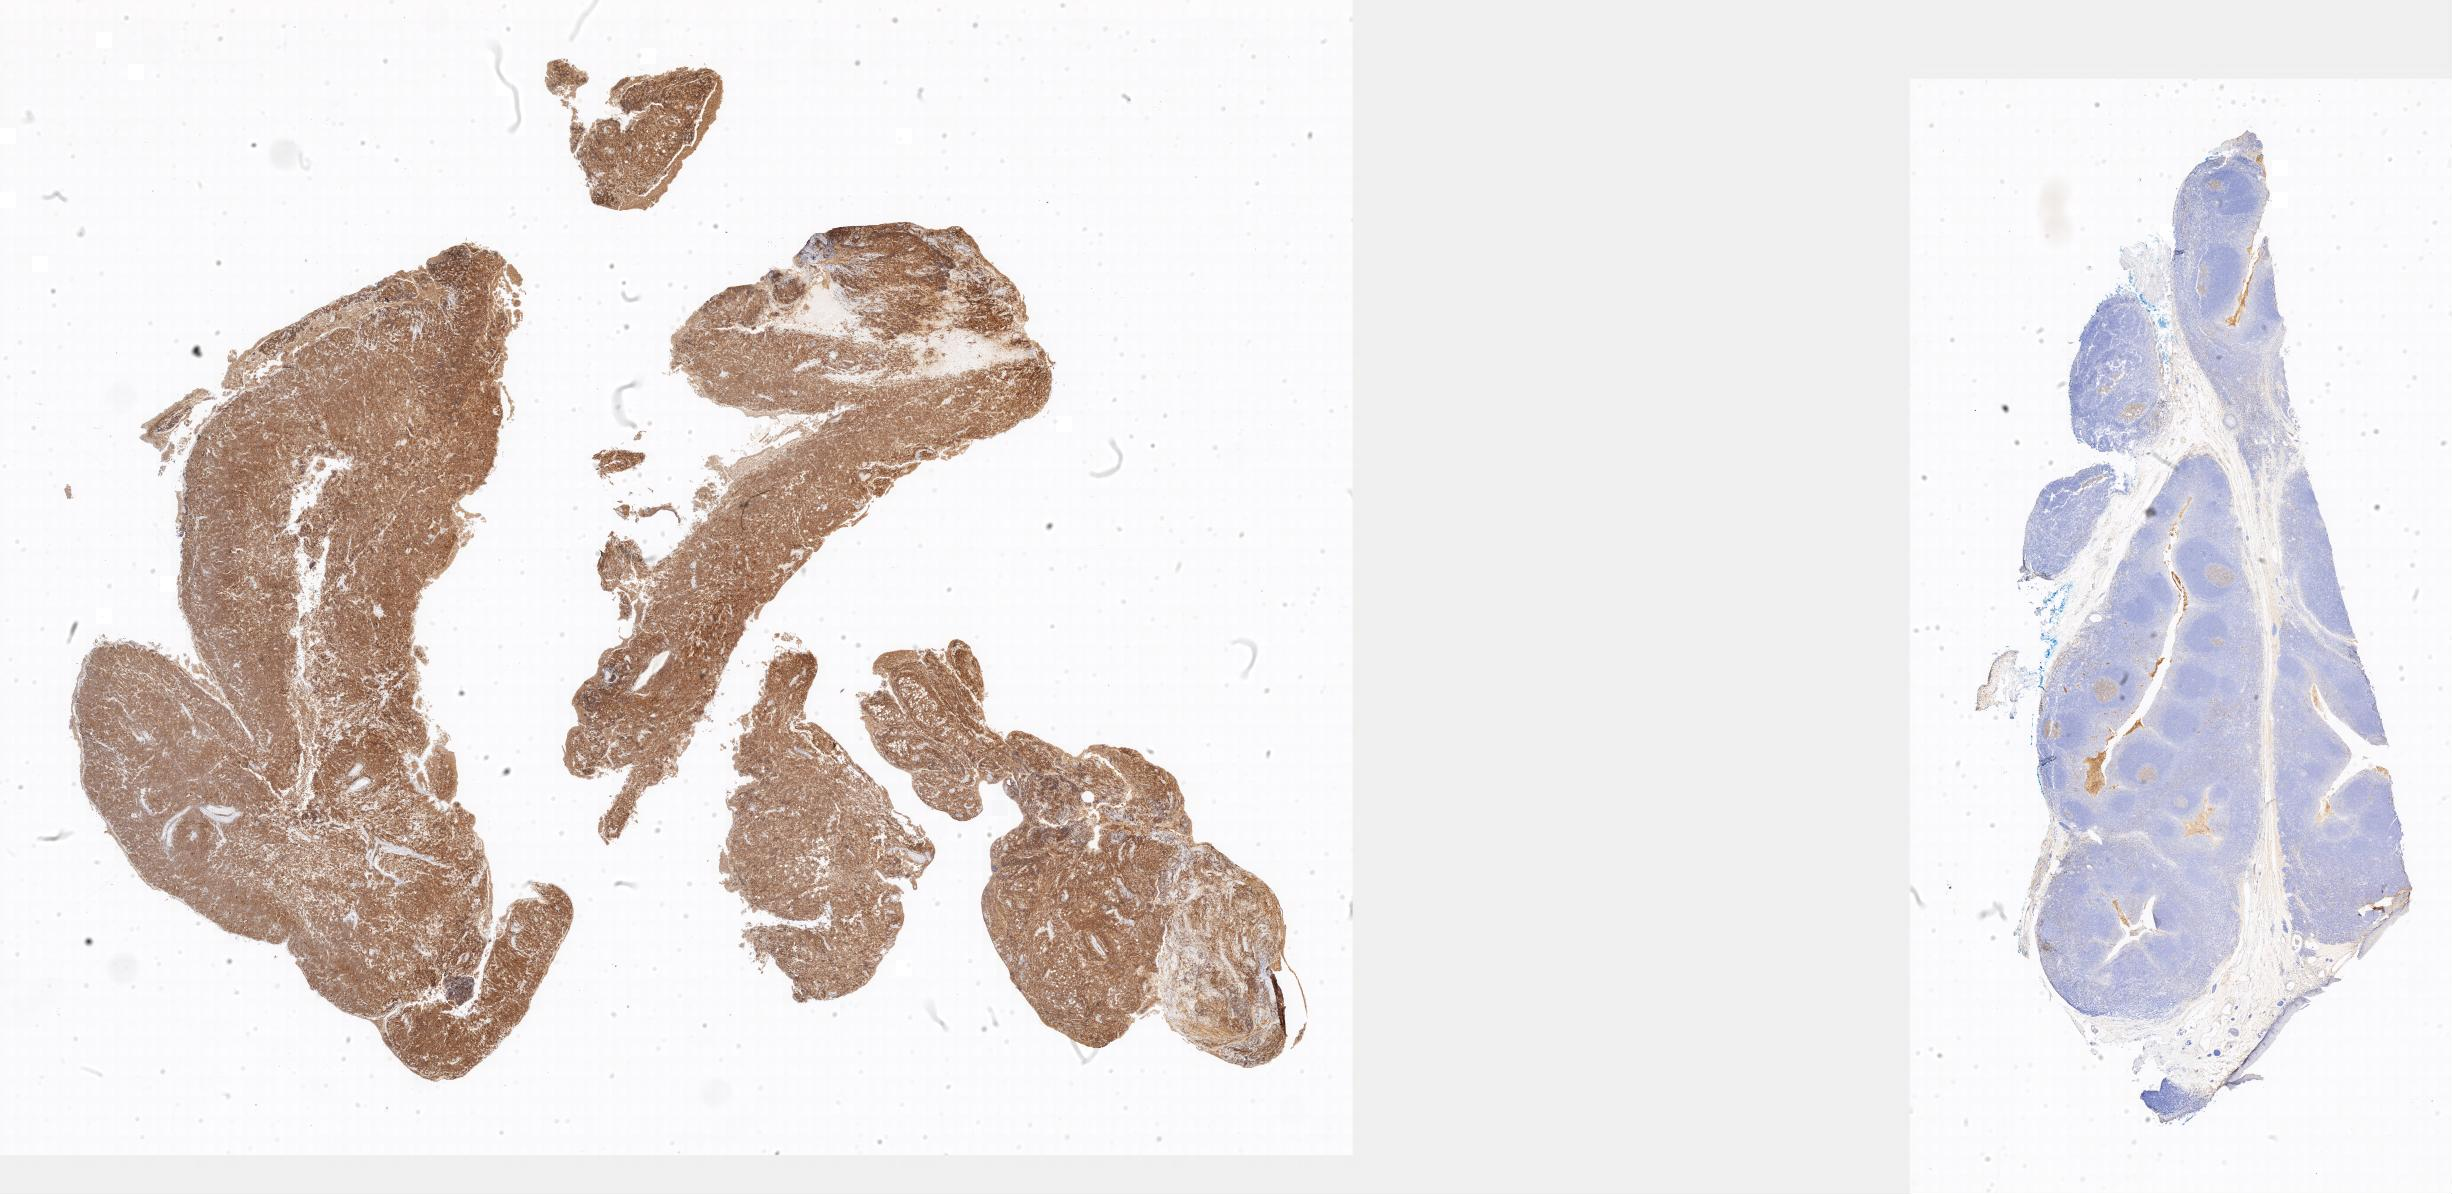
IHC for CD10, whole-slide image, a low-resolution overview of the entire scanned area; tumor tissue; site: abdomen proper. Patient: male, age at initial diagnosis 5 years.
Histologic diagnosis: Burkitt lymphoma, NOS.